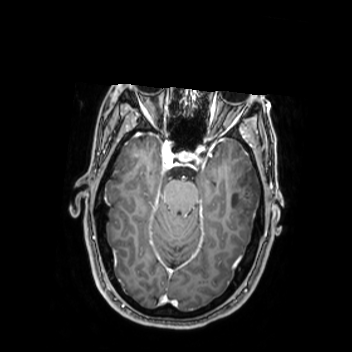
Brain MRI from a brain-tumour surgery series, one axial slice; slice 167 of 350 in the series (ordered by position); T1-weighted post-contrast; 0.9 mm slice thickness; 352 × 352 image matrix, field of view 280 × 280 mm. Case-level facts recorded for this patient, not image findings: histopathology: Oligodendroglioma; WHO grade: 2; IDH mutation: yes; tumour location: Left Middle Temporal Gyrus.
Annotated regions visible in this slice (outlined manually by an expert reader):
- tumour: bounding box <224,163,262,224> (left, top, right, bottom; pixels)